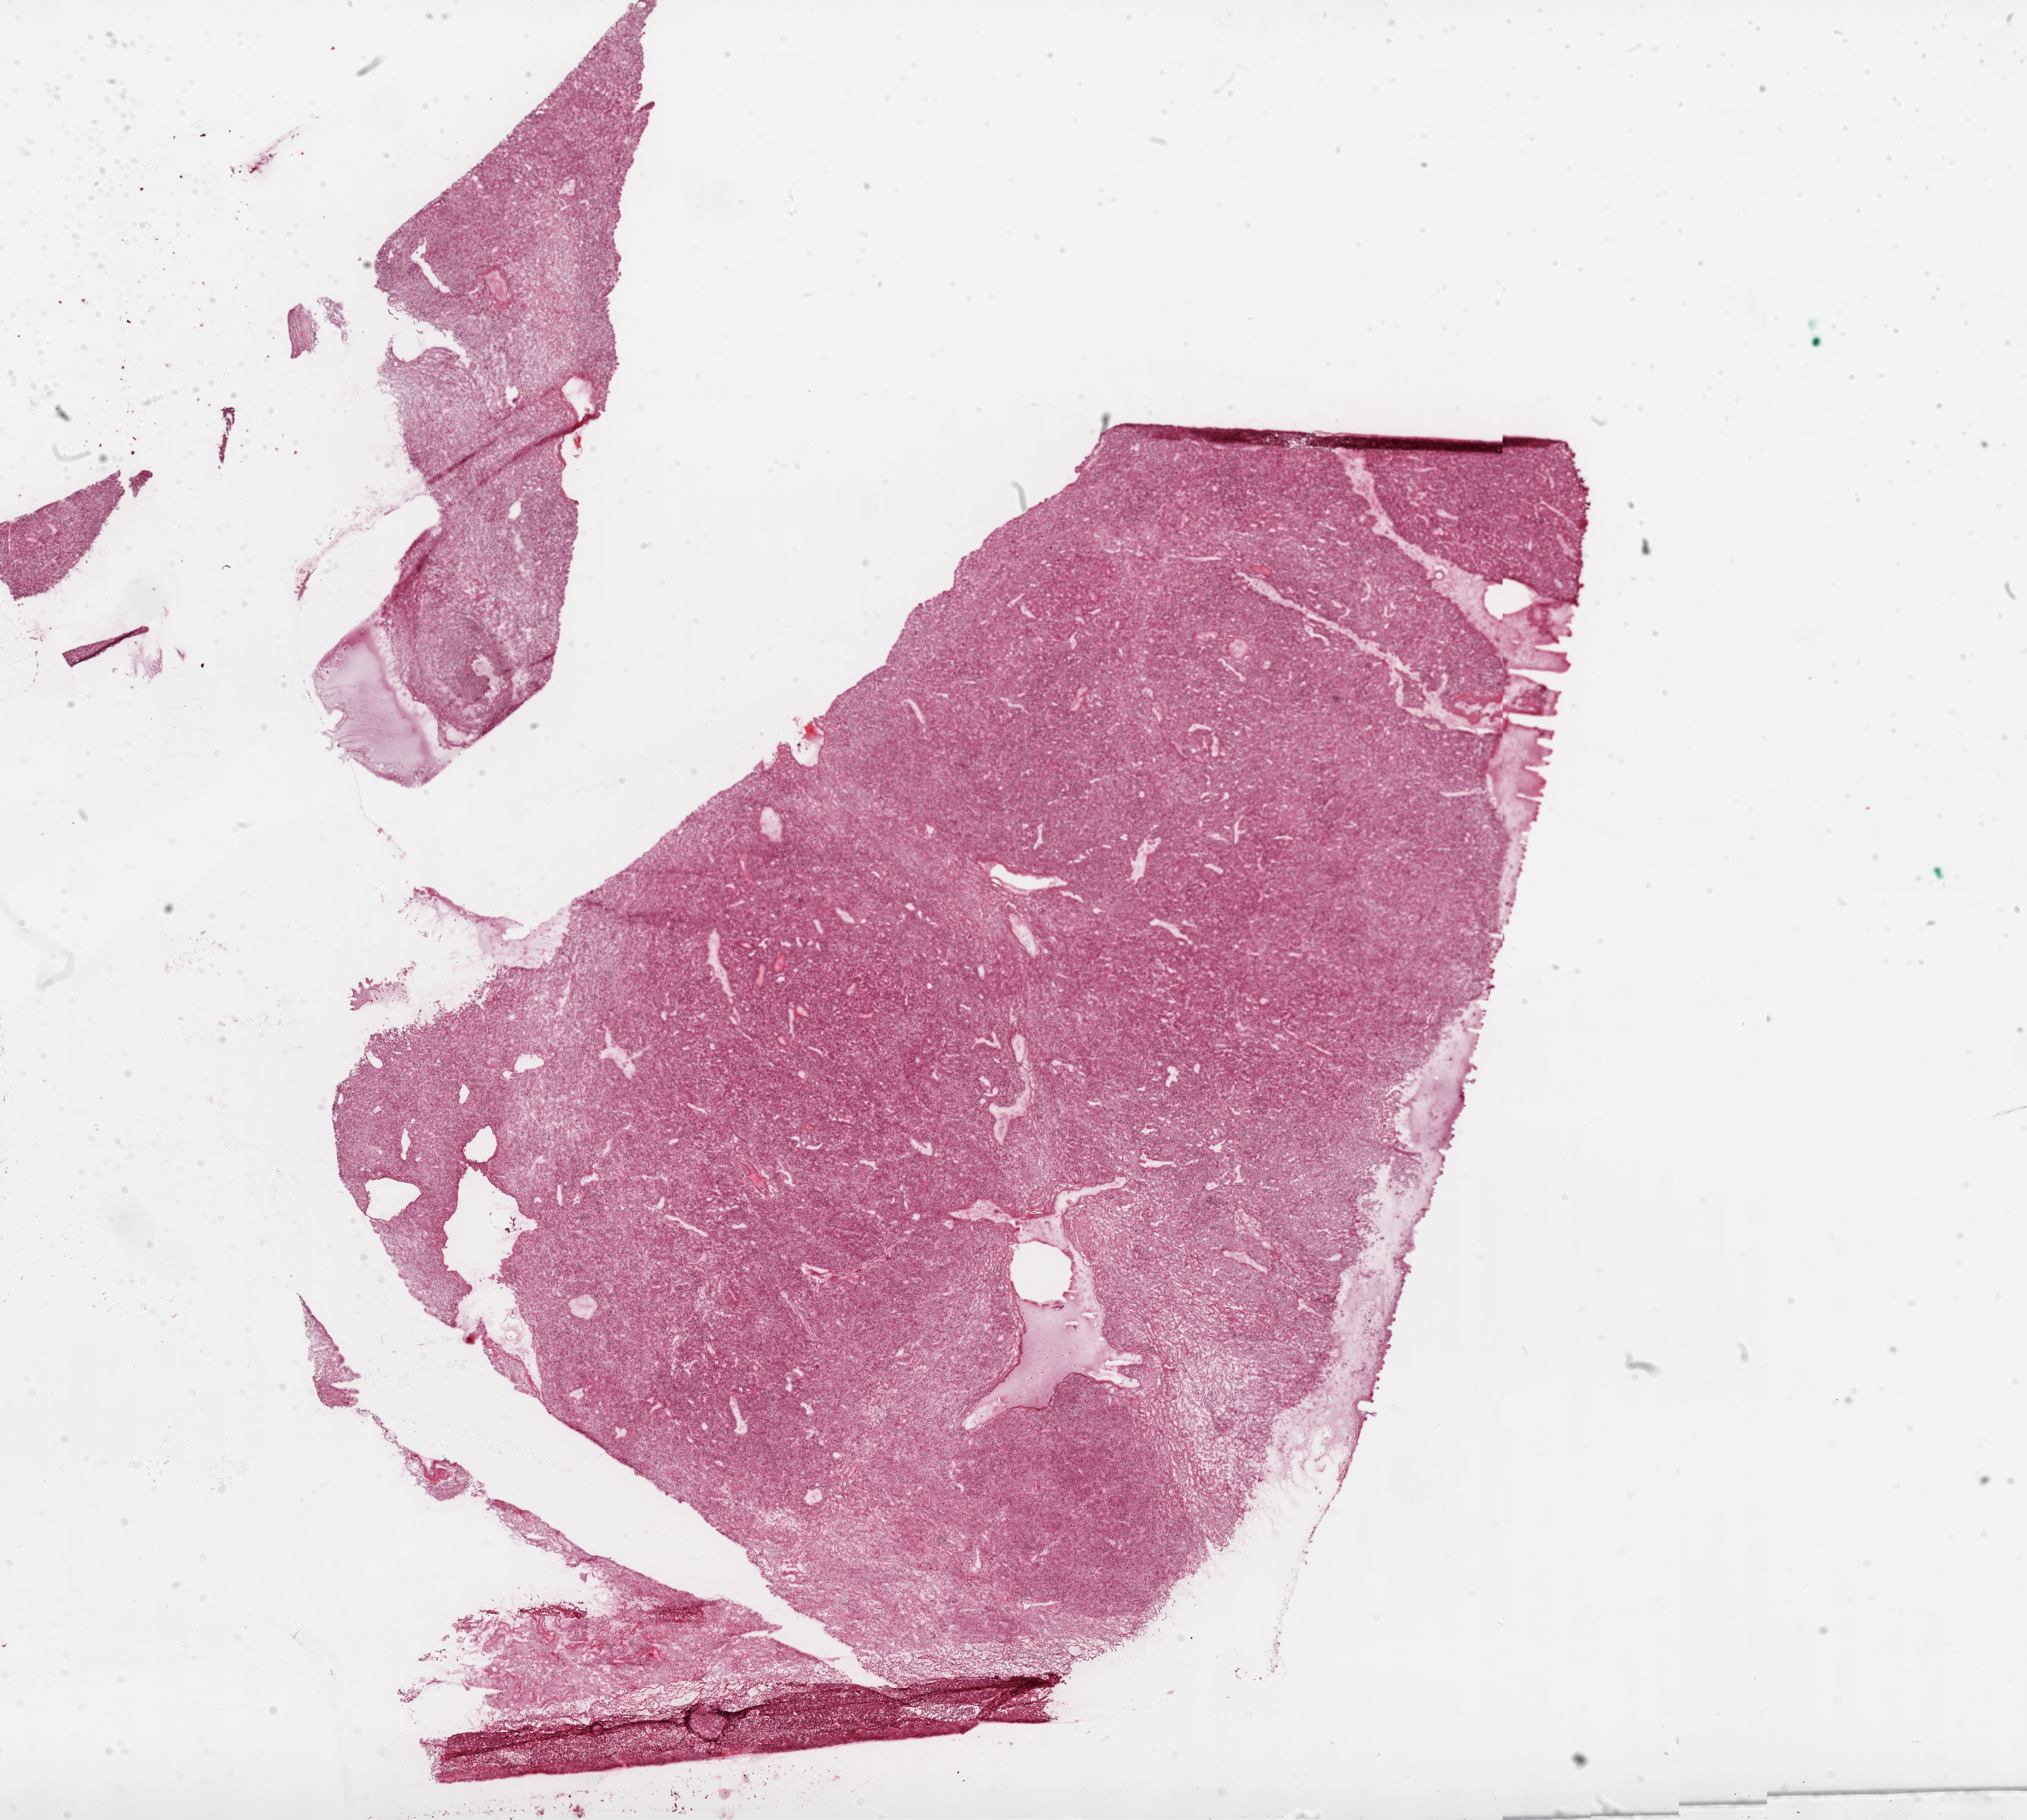
H&E-stained whole-slide image — shown as a low-resolution overview of the whole scanned area (about 23.1 x 20.7 mm, acquisition: 20x scan); frozen section from the top of the tissue portion; kidney, primary tumour sample. Female patient; age at initial diagnosis 75 years. Histologic grade: G3 (poorly differentiated). Pathologist review of this section (percent, as recorded): tumour cells 90%, tumour nuclei 85%, normal cells 0%, stromal cells 10%, necrosis 0%.
TNM: T3a NX M0. AJCC pathologic stage: III. Histologic diagnosis: Clear cell adenocarcinoma, NOS.